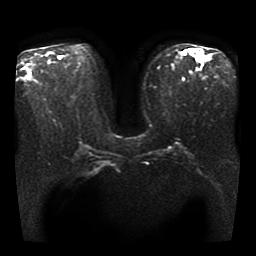
Breast MRI, one axial slice; position 20 of 40 along the scan axis; diffusion-weighted series; image 2 of 4 stored at this slice position (different b-values; order by instance number); 1.5 T; 5 mm slice thickness; 256 × 256 image matrix. Female patient.
Structures marked on this image (manually delineated by an expert):
- tumour on diffusion-weighted imaging: bounding box <198,54,202,59> (left, top, right, bottom; pixels)